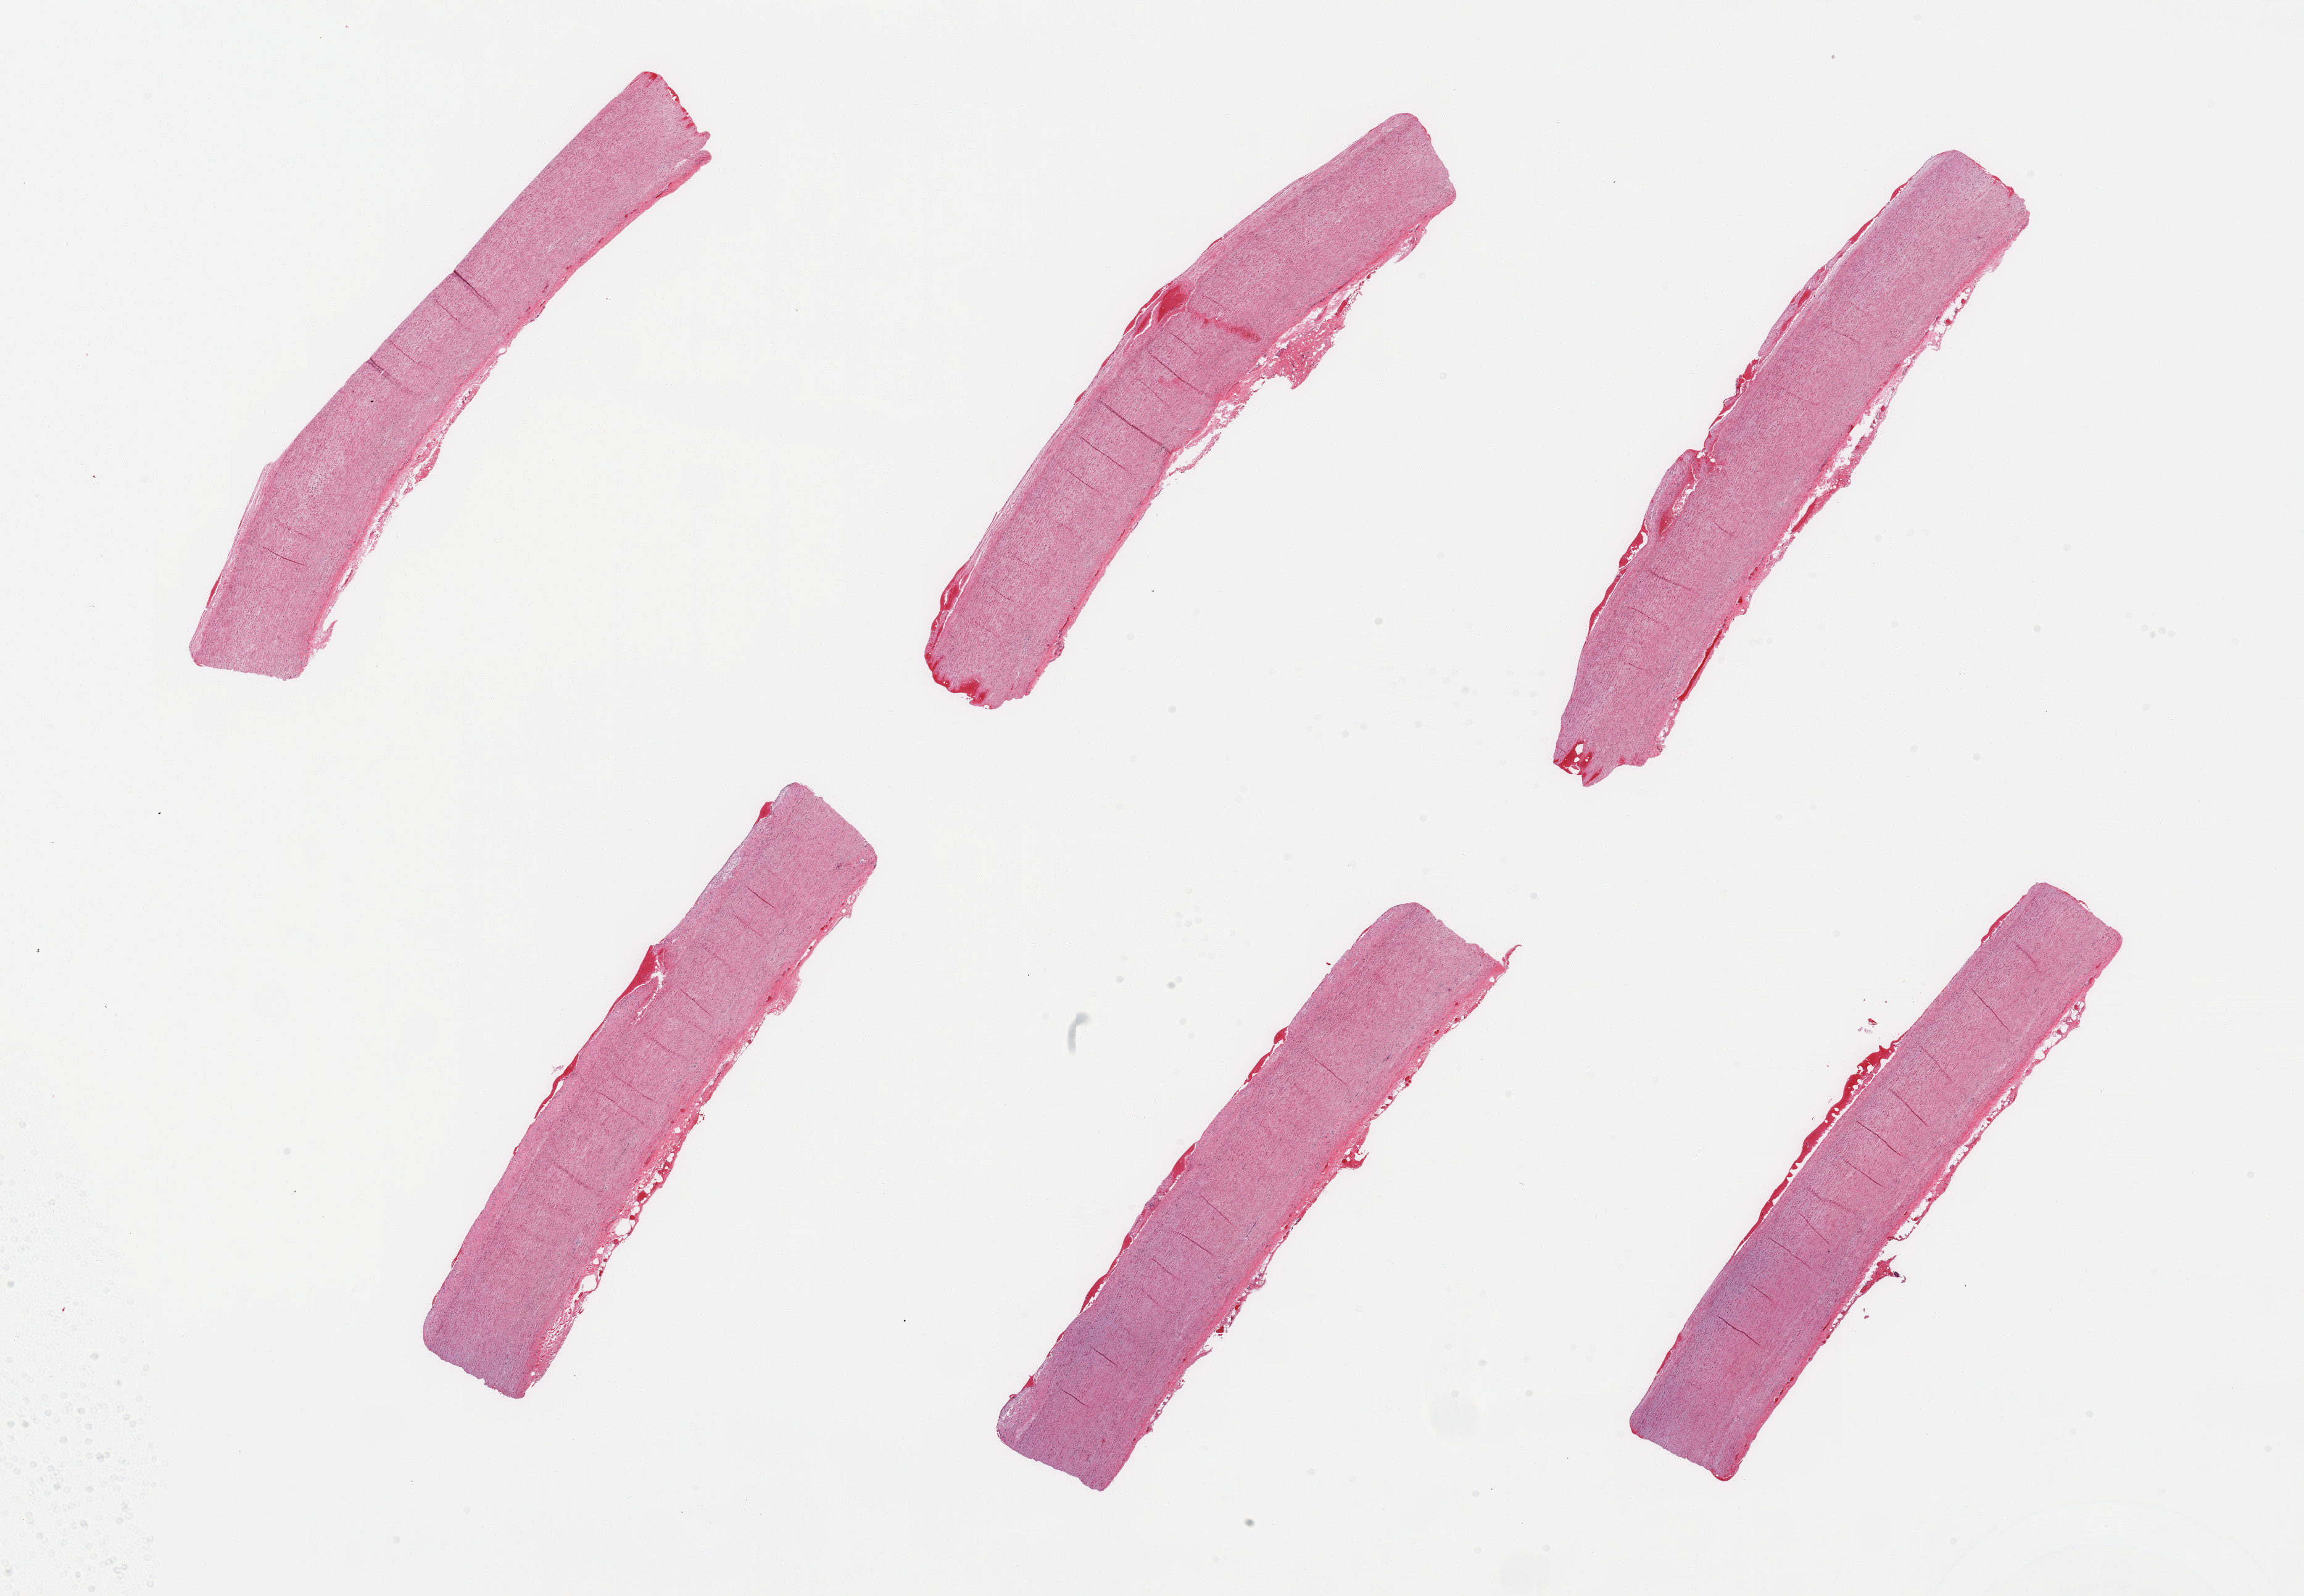
Digitized hematoxylin and eosin (H&E)-stained section — low-resolution overview of the scanned area, about 29.5 x 20.5 mm (from a 20x scan). PAXgene-fixed paraffin-embedded (PFPE) section. Target tissue: aorta. Tissue donor sample. Donor sex: female.
Reviewer comment on this tissue sample: 6 pieces; atherosclerosis.